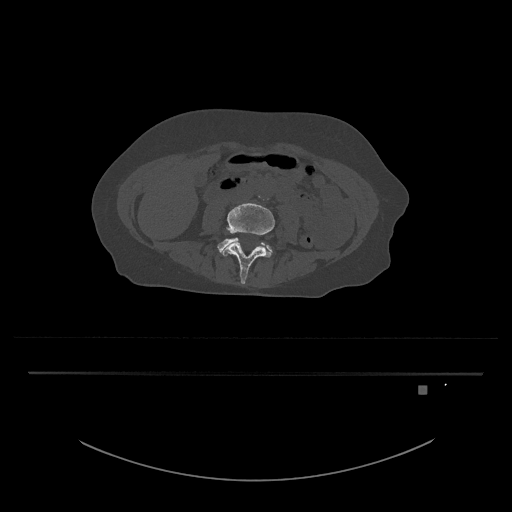
CT including the spine, one axial slice; slice 349 of 797 in the series (ordered by position); reconstruction kernel Br40s/3; 120 kVp; bone window (W 1800 / L 400 HU); 0.5 mm slice thickness; 512 × 512 image matrix, field of view 500 × 500 mm. Female patient, age 57 years. Case-level facts recorded for this patient, not image findings: primary cancer: cervical.
Annotated regions visible in this slice (semi-automatically segmented with operator editing):
- L4 vertebra: bounding box <220,203,275,284> (left, top, right, bottom; pixels)